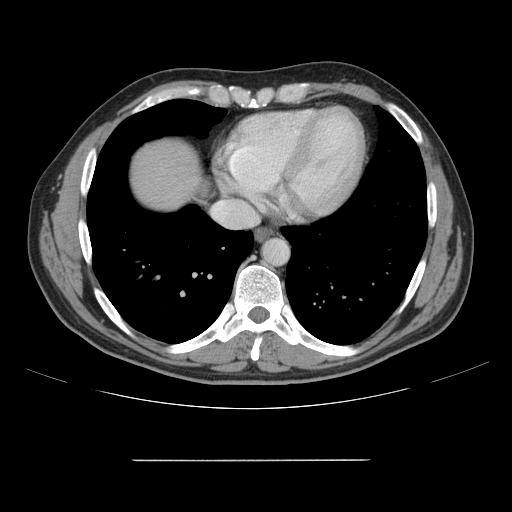
Contrast-enhanced abdominal CT, one axial slice. Position 148 of 164 along the scan axis. 120 kVp. Intravenous contrast given. Soft-tissue window (W 400 / L 40 HU). 2.5 mm slice thickness. 512 × 512 image matrix, field of view 404 × 404 mm. Male patient, age 54 years. From the clinical record (not read from this slice): diagnosis: colorectal cancer liver metastases, imaged before liver resection; multiple liver metastases: yes; largest metastasis: 1 cm; disease in both lobes: no.
Annotated regions visible in this slice (expert manual segmentation):
- hepatic veins: bounding box <212,200,258,225> (left, top, right, bottom; pixels)
- liver: <131,141,199,208>
- planned liver remnant (the part of the liver to remain after resection): <131,140,199,208>